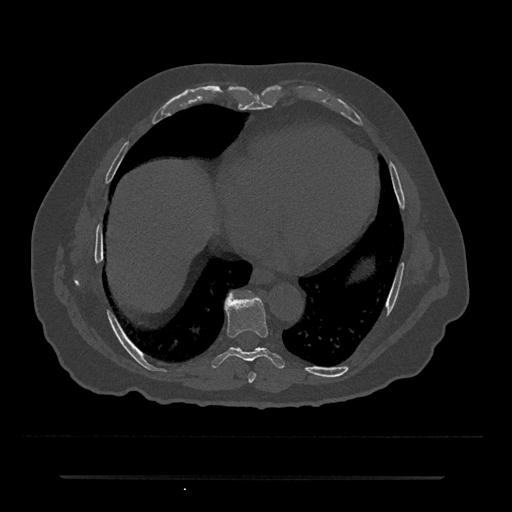
CT including the spine, one axial slice. Slice 328 of 797 in the series (ordered by position). Reconstruction kernel Br40s/3. 120 kVp. Bone window (W 1800 / L 400 HU). 0.5 mm slice thickness. 512 × 512 image matrix, field of view 437 × 437 mm. Male patient, age 69 years. From the clinical record (not read from this slice): primary cancer: prostate.
Annotated regions visible in this slice (semi-automatic segmentation, software-assisted and operator-edited):
- T7 vertebra: box from (x=248, y=372) to (x=256, y=383) px
- T8 vertebra: (x=212, y=294)–(x=285, y=369)